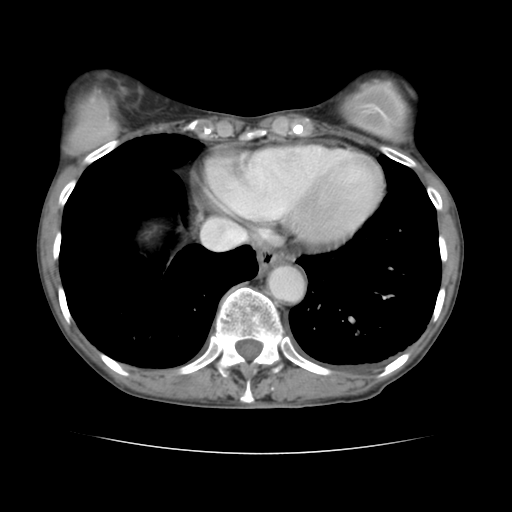
Contrast-enhanced abdominal CT, one axial slice. 120 kVp. Intravenous contrast given. Soft-tissue window (W 400 / L 40 HU). 2.5 mm slice thickness. 512 × 512 image matrix, field of view 319 × 319 mm. Female patient, age 77 years. From the clinical record (not read from this slice): diagnosis: colorectal cancer liver metastases, imaged before liver resection; multiple liver metastases: yes; largest metastasis: 3 cm; disease in both lobes: no.
Annotated regions visible in this slice (outlined manually by an expert reader):
- hepatic veins: box from (x=202, y=220) to (x=247, y=250) px